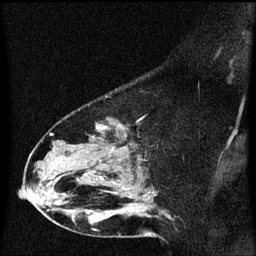
Breast MRI (dynamic contrast-enhanced), one sagittal slice. Slice 39 of 60 in the series (ordered by position). Dynamic contrast-enhanced series, image 2 of 3 at this slice position (ordered by acquisition). 1.5 T. TE 4.2 ms, TR 8.4 ms. 256 × 256 image matrix, field of view 200 × 200 mm. Female patient, age 49 years. Case-level facts recorded for this patient, not image findings: setting: breast cancer imaged before/during neoadjuvant chemotherapy; receptor status: HR-positive, HER2-negative.
Annotated regions visible in this slice (semi-automatically segmented with operator editing):
- analysis volume of interest (the breast-tissue region the enhancement analysis was run in; not a lesion): bounding box <27,104,171,221> (left, top, right, bottom; pixels)
- tumour enhancement mask (voxels above the 70 % enhancement threshold inside the analysis volume of interest): <118,126,121,129>